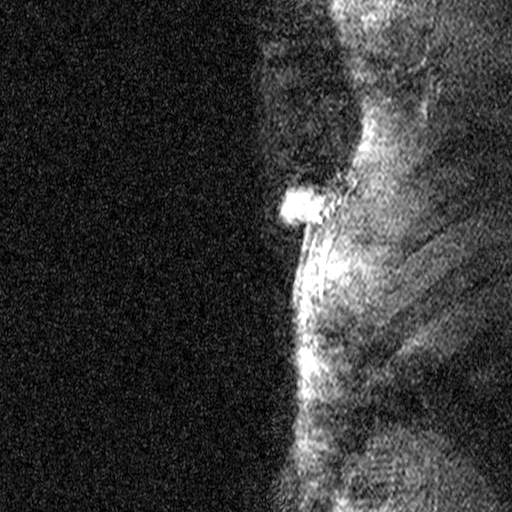
Breast MRI (dynamic contrast-enhanced), one sagittal slice; position 39 of 44 along the scan axis; dynamic contrast-enhanced study with each time point stored as its own series, time point 2 of 3 at this slice position (early post-contrast, ordered by acquisition time); 1.5 T; TE 4.5 ms, TR 11 ms; 512 × 512 image matrix, field of view 200 × 200 mm. Patient: female, 44 years. Case-level facts recorded for this patient, not image findings: setting: breast cancer imaged before/during neoadjuvant chemotherapy; receptor status: HR-positive, HER2-negative.
Annotated regions visible in this slice (semi-automatically segmented with operator editing):
- analysis volume of interest (the breast-tissue region the enhancement analysis was run in; not a lesion): bounding box (x1, y1, x2, y2) in pixels: (218, 118, 341, 291)
- tumour enhancement mask (voxels above the 90 % enhancement threshold inside the analysis volume of interest): (278, 186, 339, 272)